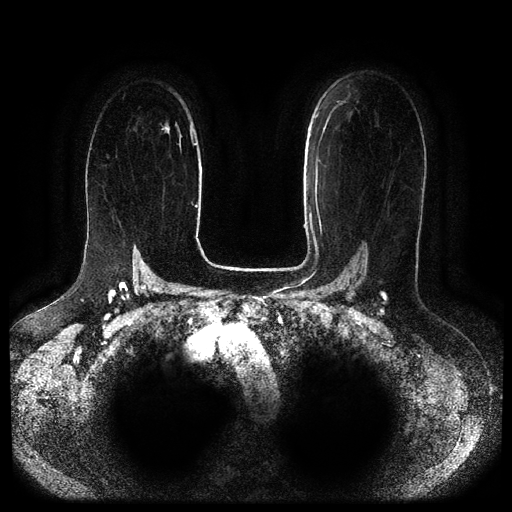
Breast MRI (dynamic contrast-enhanced, multi-phase), one axial slice. Slice 66 of 116 in the series (ordered by position). Dynamic contrast-enhanced series, time point 2 of 5 at this slice position (early post-contrast). 1.5 T. TE 2.6 ms, TR 5.3 ms. 2.1 mm slice thickness. 512 × 512 image matrix. Patient: female, 65 years.
Annotated regions visible in this slice (semi-automatically segmented with operator editing):
- breast lesion (labelled benign in the annotation): bounding box <161,123,170,133> (left, top, right, bottom; pixels)